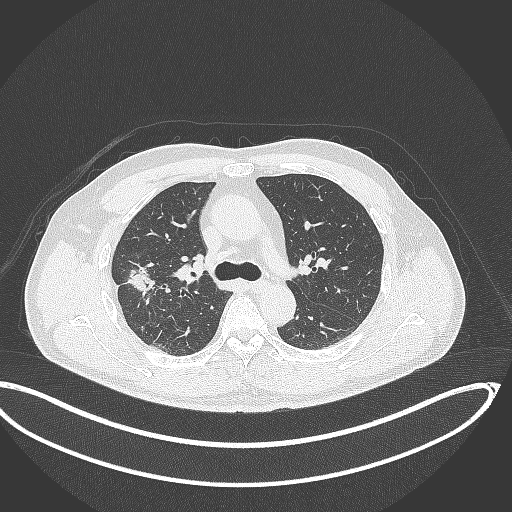
Chest CT, one axial slice. Lung window (W 1500 / L -600 HU). 1 mm slice thickness. 512 × 512 image matrix. Male patient, age 63 years. From the clinical record (not read from this slice): clinical TNM (as recorded): T1c N0 M0.
Outlined on this slice (bounding box drawn by a radiologist):
- lung tumour (recorded histology: adenocarcinoma): bounding box (x1, y1, x2, y2) in pixels: (122, 259, 164, 301)